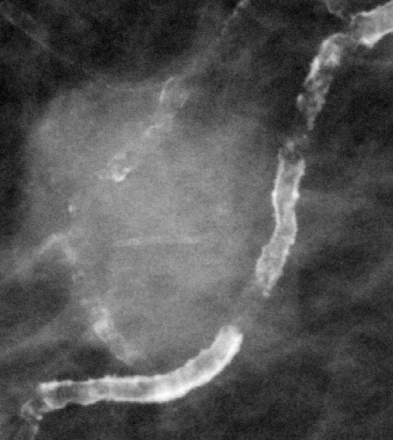
Region of interest cut from a scanned film mammogram (one marked finding); right breast; MLO view; BI-RADS breast density category 1 (scale 1–4).
Marked abnormality: mass, shape irregular, margins microlobulated; BI-RADS assessment category 5; subtlety rating 5 on a 1 (subtle) to 5 (obvious) scale; pathology result (as recorded, not read from the image): malignant.